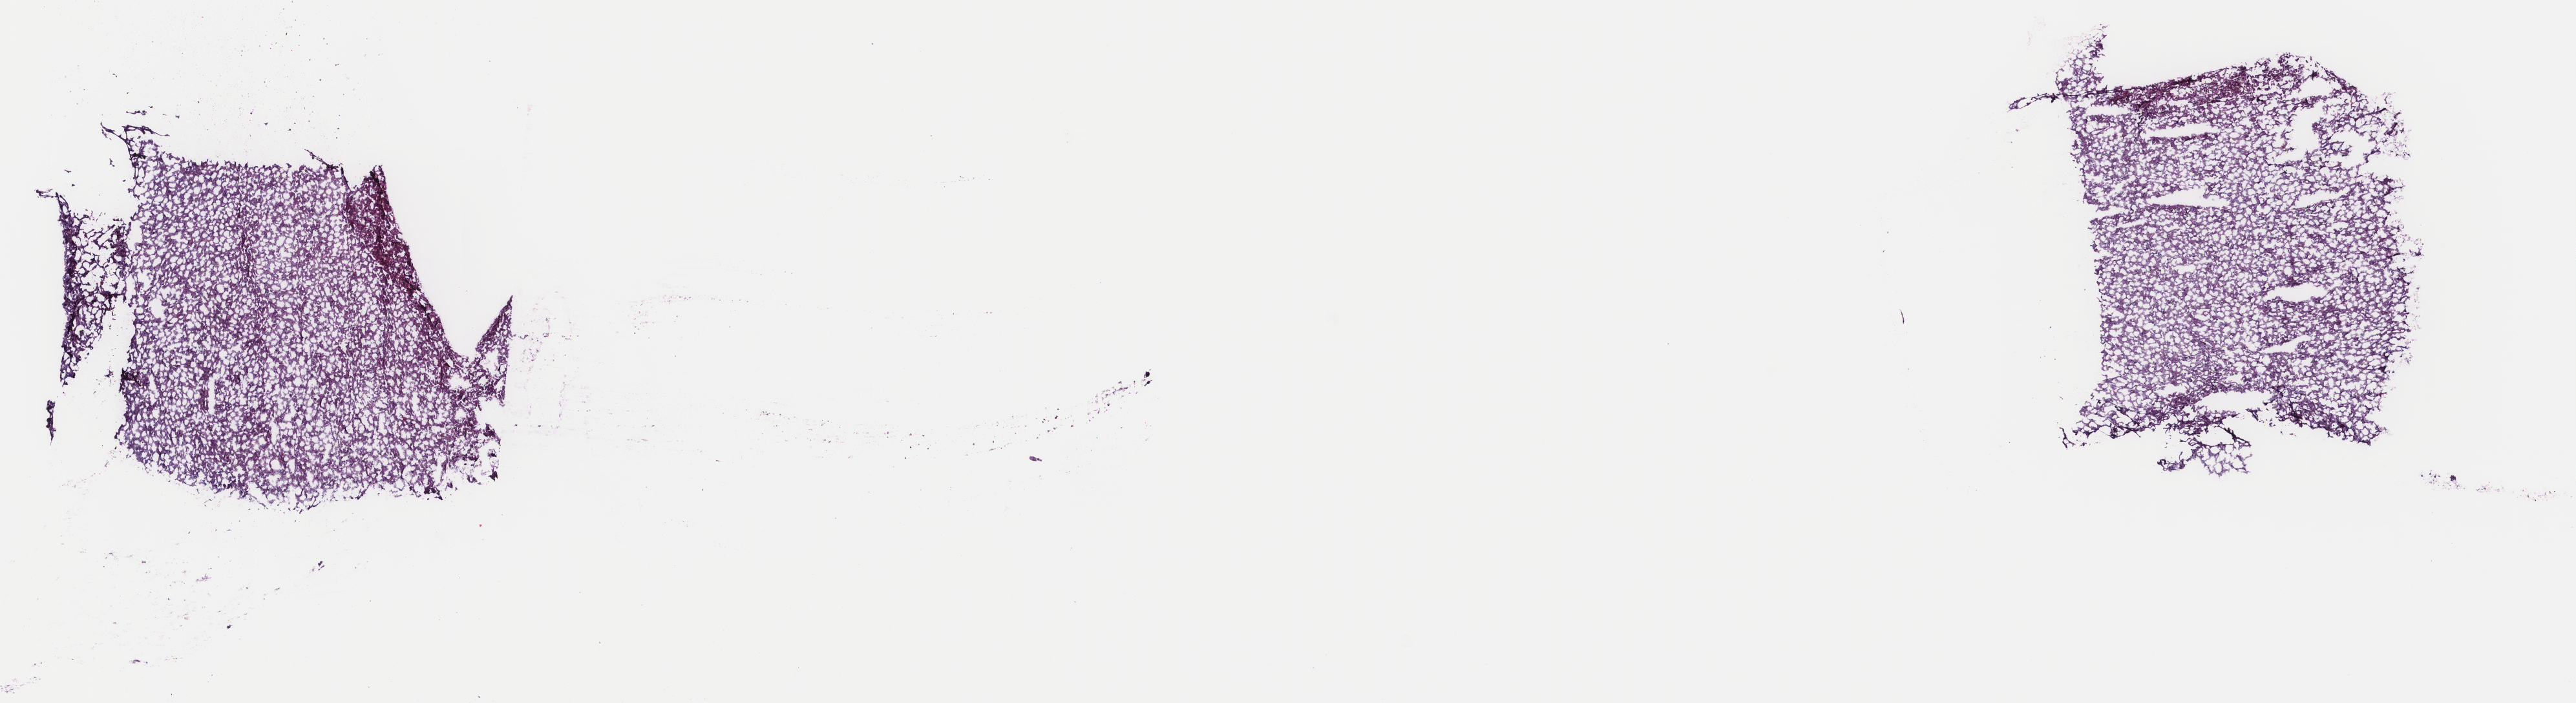
Digitized H&E-stained tissue section (whole slide) — shown as a low-resolution overview of the whole scanned area (about 15.8 x 4.3 mm); frozen section from the top of the tissue portion; primary tumour sample from the brain. Male patient; age at initial diagnosis 86 years. Histologic grade: G2 (moderately differentiated). Composition of this section per pathologist review: tumour cells 10%, tumour nuclei 75%, normal cells 5%, stromal cells 85%, necrosis 0%. Infiltration values recorded for this section: lymphocyte infiltration 0%, monocyte infiltration 0%, neutrophil infiltration 0%.
* pathologic diagnosis: Oligodendroglioma, NOS (cerebrum)